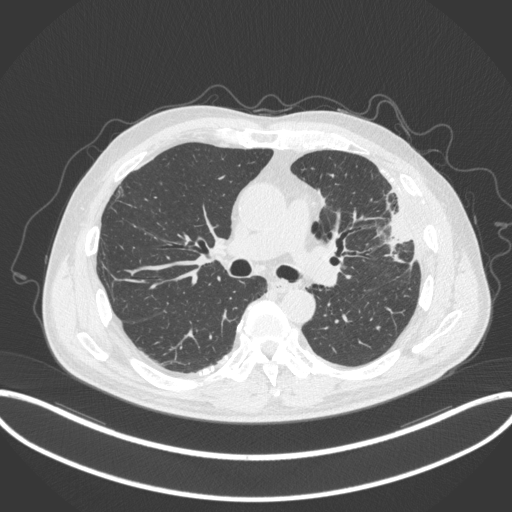
Chest CT, one axial slice; slice 201 of 382 in the series (ordered by position); reconstruction kernel B31f; 120 kVp; lung window (W 1500 / L -600 HU); 1 mm slice thickness; 512 × 512 image matrix, field of view 415 × 415 mm. Male patient, age 64 years. Case-level facts recorded for this patient, not image findings: clinical TNM (as recorded): T4 N1 M0; histopathological grade: G3.
Annotated regions visible in this slice (rectangle marked by the reading radiologist):
- lung tumour (recorded histology: adenocarcinoma): bounding box (x1, y1, x2, y2) in pixels: (376, 189, 421, 264)